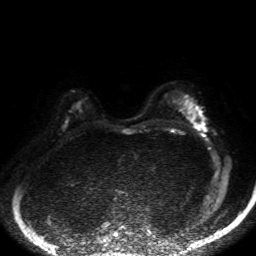
Breast MRI, one axial slice. Position 33 of 50 along the scan axis. Diffusion-weighted series; image 2 of 4 stored at this slice position (different b-values; order by instance number). 1.5 T. 4 mm slice thickness. 256 × 256 image matrix, field of view 320 × 320 mm. Female patient.
Annotated regions visible in this slice (manually delineated by an expert):
- tumour on diffusion-weighted imaging: box from (x=192, y=118) to (x=205, y=127) px